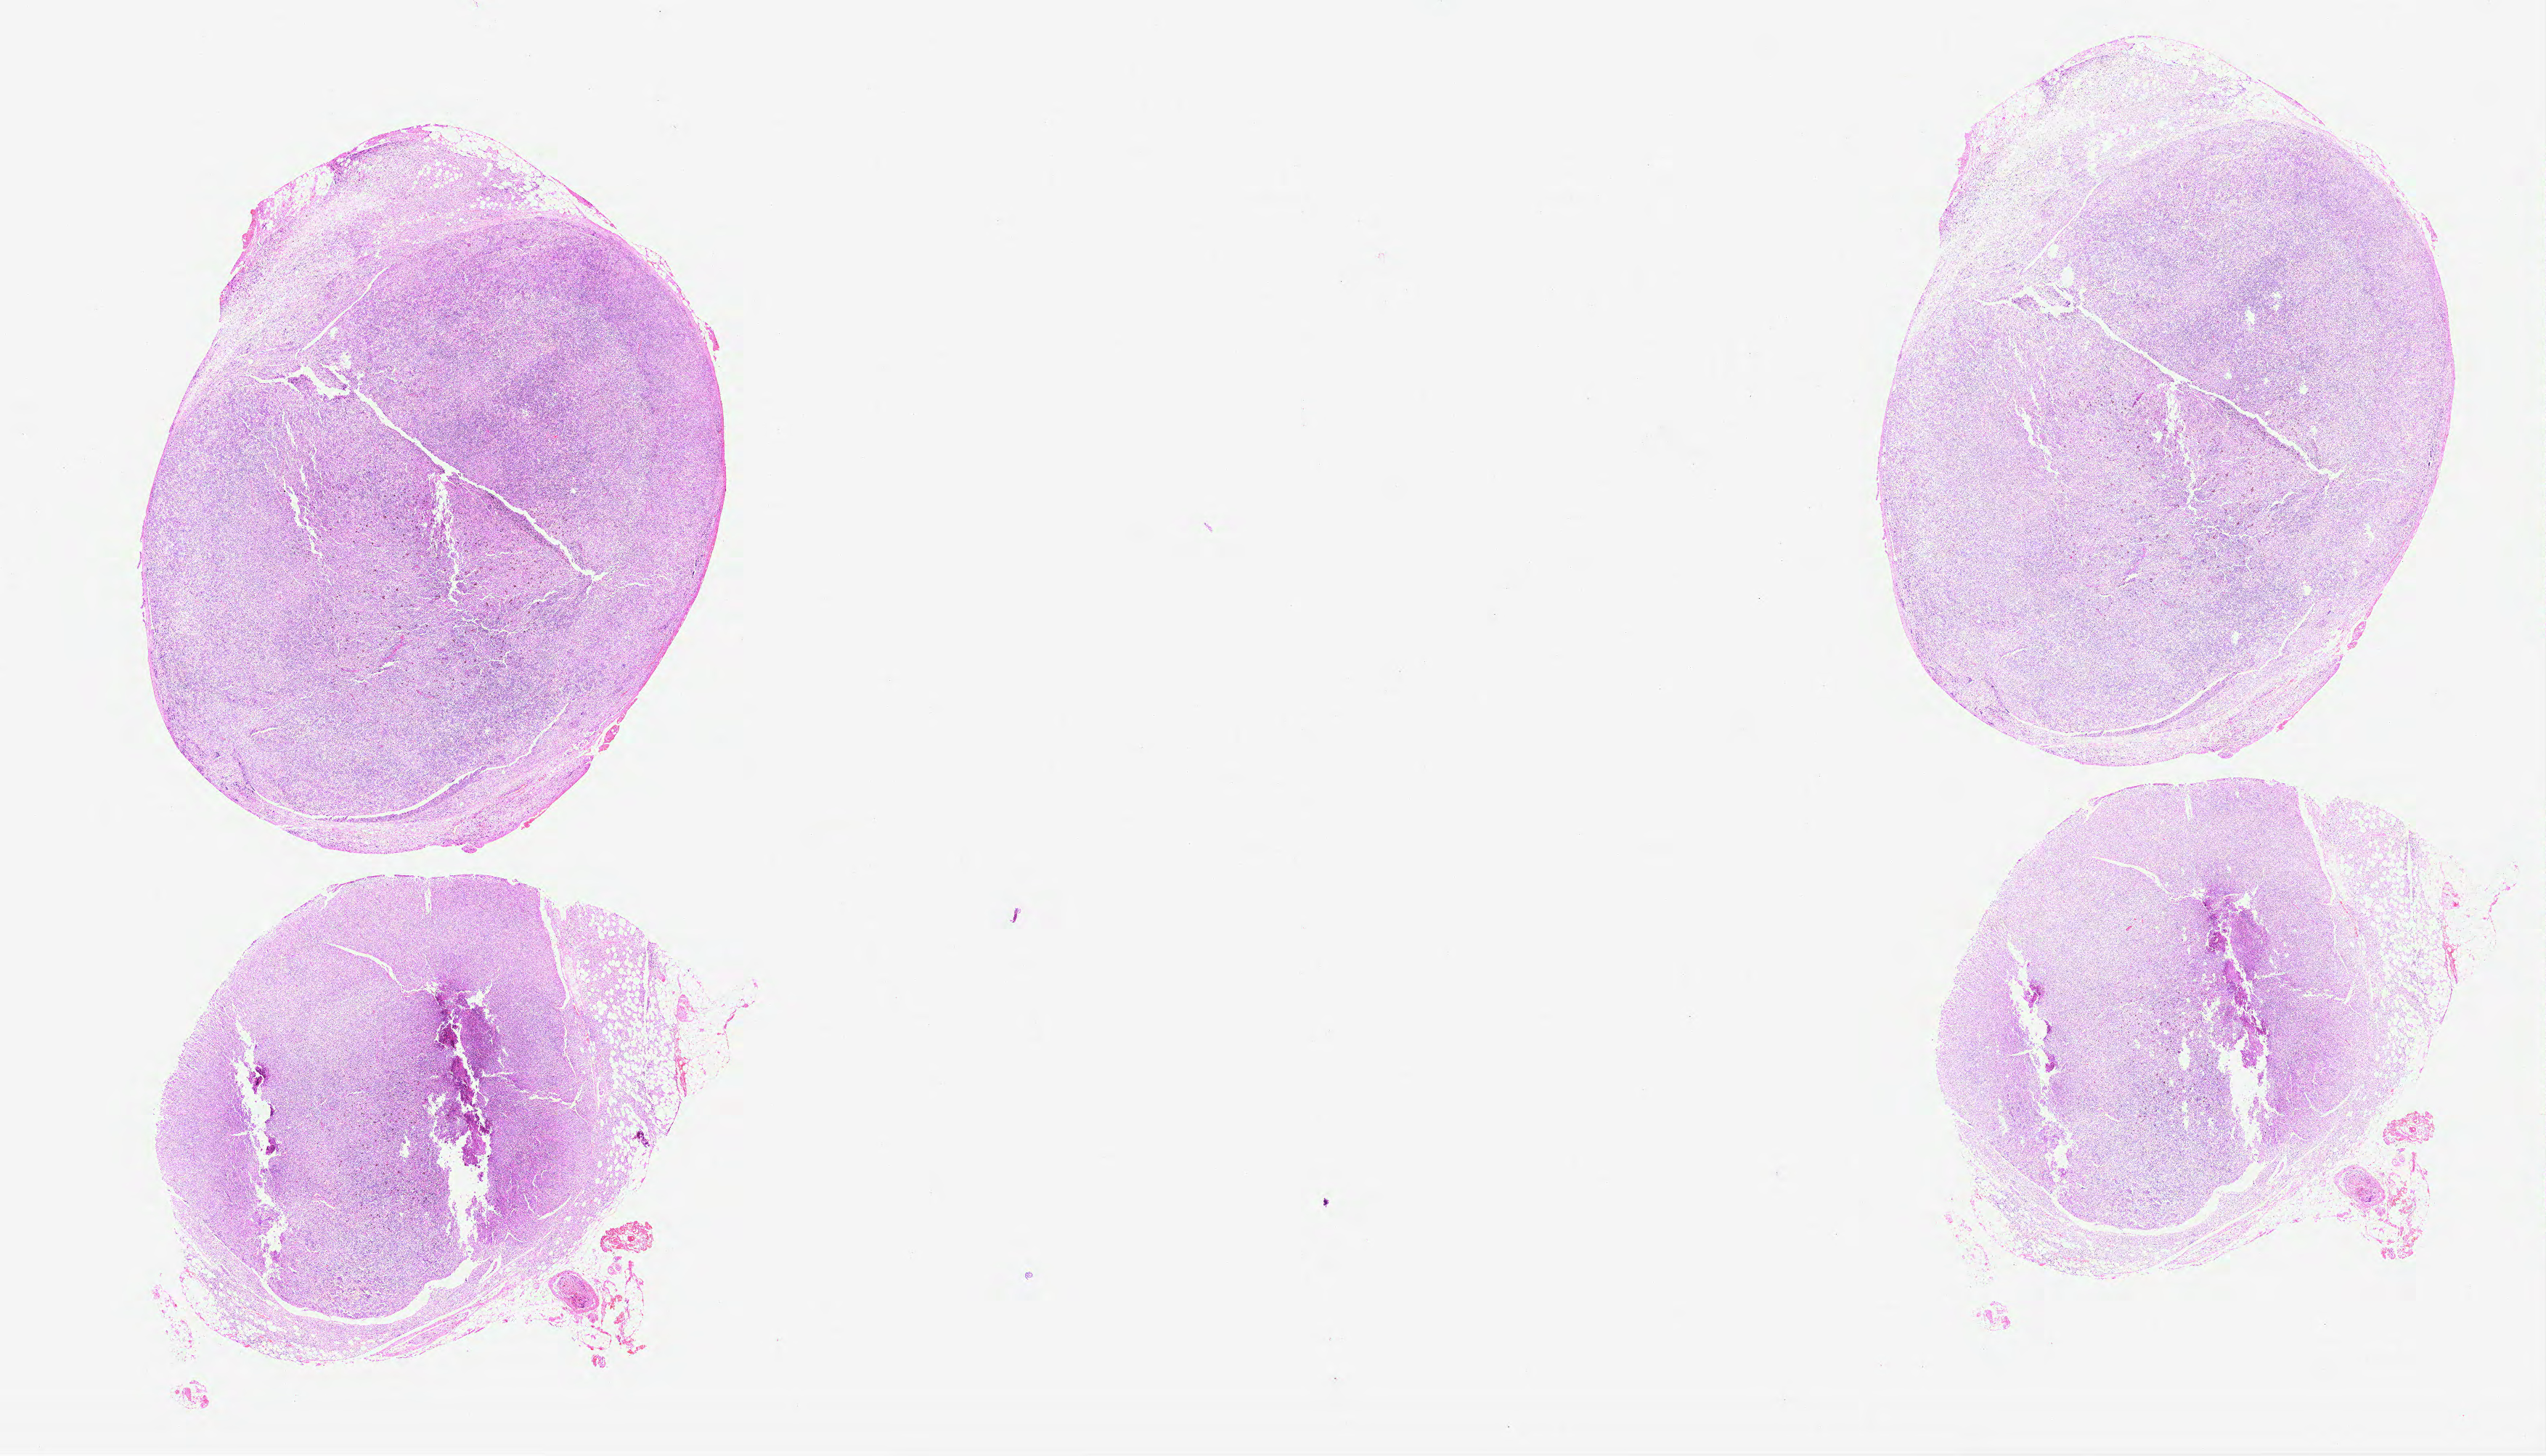
Digitized Hematoxylin and eosin (H&E) stained tissue section (whole slide), shown as a low-resolution overview of the whole scanned area (about 28.3 x 16.2 mm), formalin-fixed paraffin-embedded (FFPE) diagnostic section, sample: primary tumour, lymphoid tissue. Female, age 57 years at initial diagnosis.
Histologic diagnosis: Diffuse large B-cell lymphoma, NOS (lymph nodes of head, face and neck).